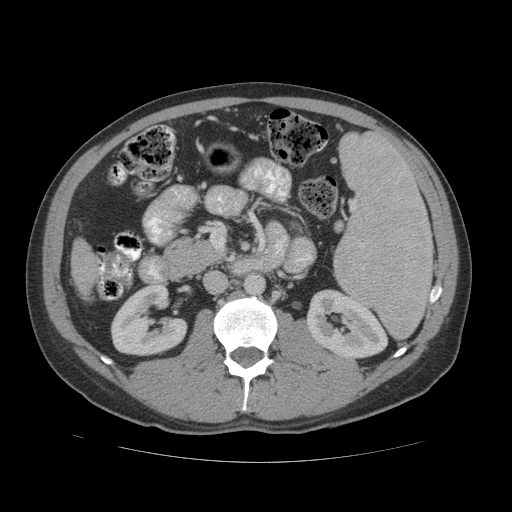
Contrast-enhanced abdominal CT (liver protocol), one axial slice; position 11 of 81 along the scan axis; 140 kVp; soft-tissue window (W 400 / L 40 HU); 2.5 mm slice thickness; 512 × 512 image matrix, field of view 400 × 400 mm. Case-level facts recorded for this patient, not image findings: diagnosis: hepatocellular carcinoma (patient treated with transarterial chemoembolisation; whether this scan precedes or follows treatment is not stated here); TNM stage (as recorded): Stage-IVB; Child-Pugh class: B; tumour nodularity: multinodular.
Outlined on this slice (semi-automatically segmented with operator editing):
- liver parenchyma outside the tumour (the mass and vessels are separate outlines, so this box may not span the whole liver): bounding box (x1, y1, x2, y2) in pixels: (70, 240, 96, 294)